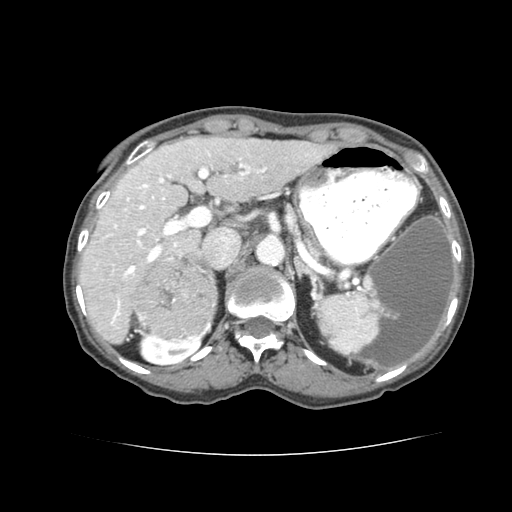
Contrast-enhanced abdominal CT (liver protocol), one axial slice. Slice 47 of 77 in the series (ordered by position). 120 kVp. Soft-tissue window (W 400 / L 40 HU). 2.5 mm slice thickness. 512 × 512 image matrix, field of view 340 × 340 mm. Case-level facts recorded for this patient, not image findings: diagnosis: hepatocellular carcinoma (patient treated with transarterial chemoembolisation; whether this scan precedes or follows treatment is not stated here); TNM stage (as recorded): Stage-I; Child-Pugh class: A; tumour differentiation: well differentiated; tumour size: 7.6 cm.
Structures marked on this image (semi-automatically segmented with operator editing):
- liver parenchyma outside the tumour (the mass and vessels are separate outlines, so this box may not span the whole liver): bounding box (x1, y1, x2, y2) in pixels: (76, 134, 338, 340)
- mass: (132, 257, 216, 338)
- liver vessels: (82, 147, 304, 311)